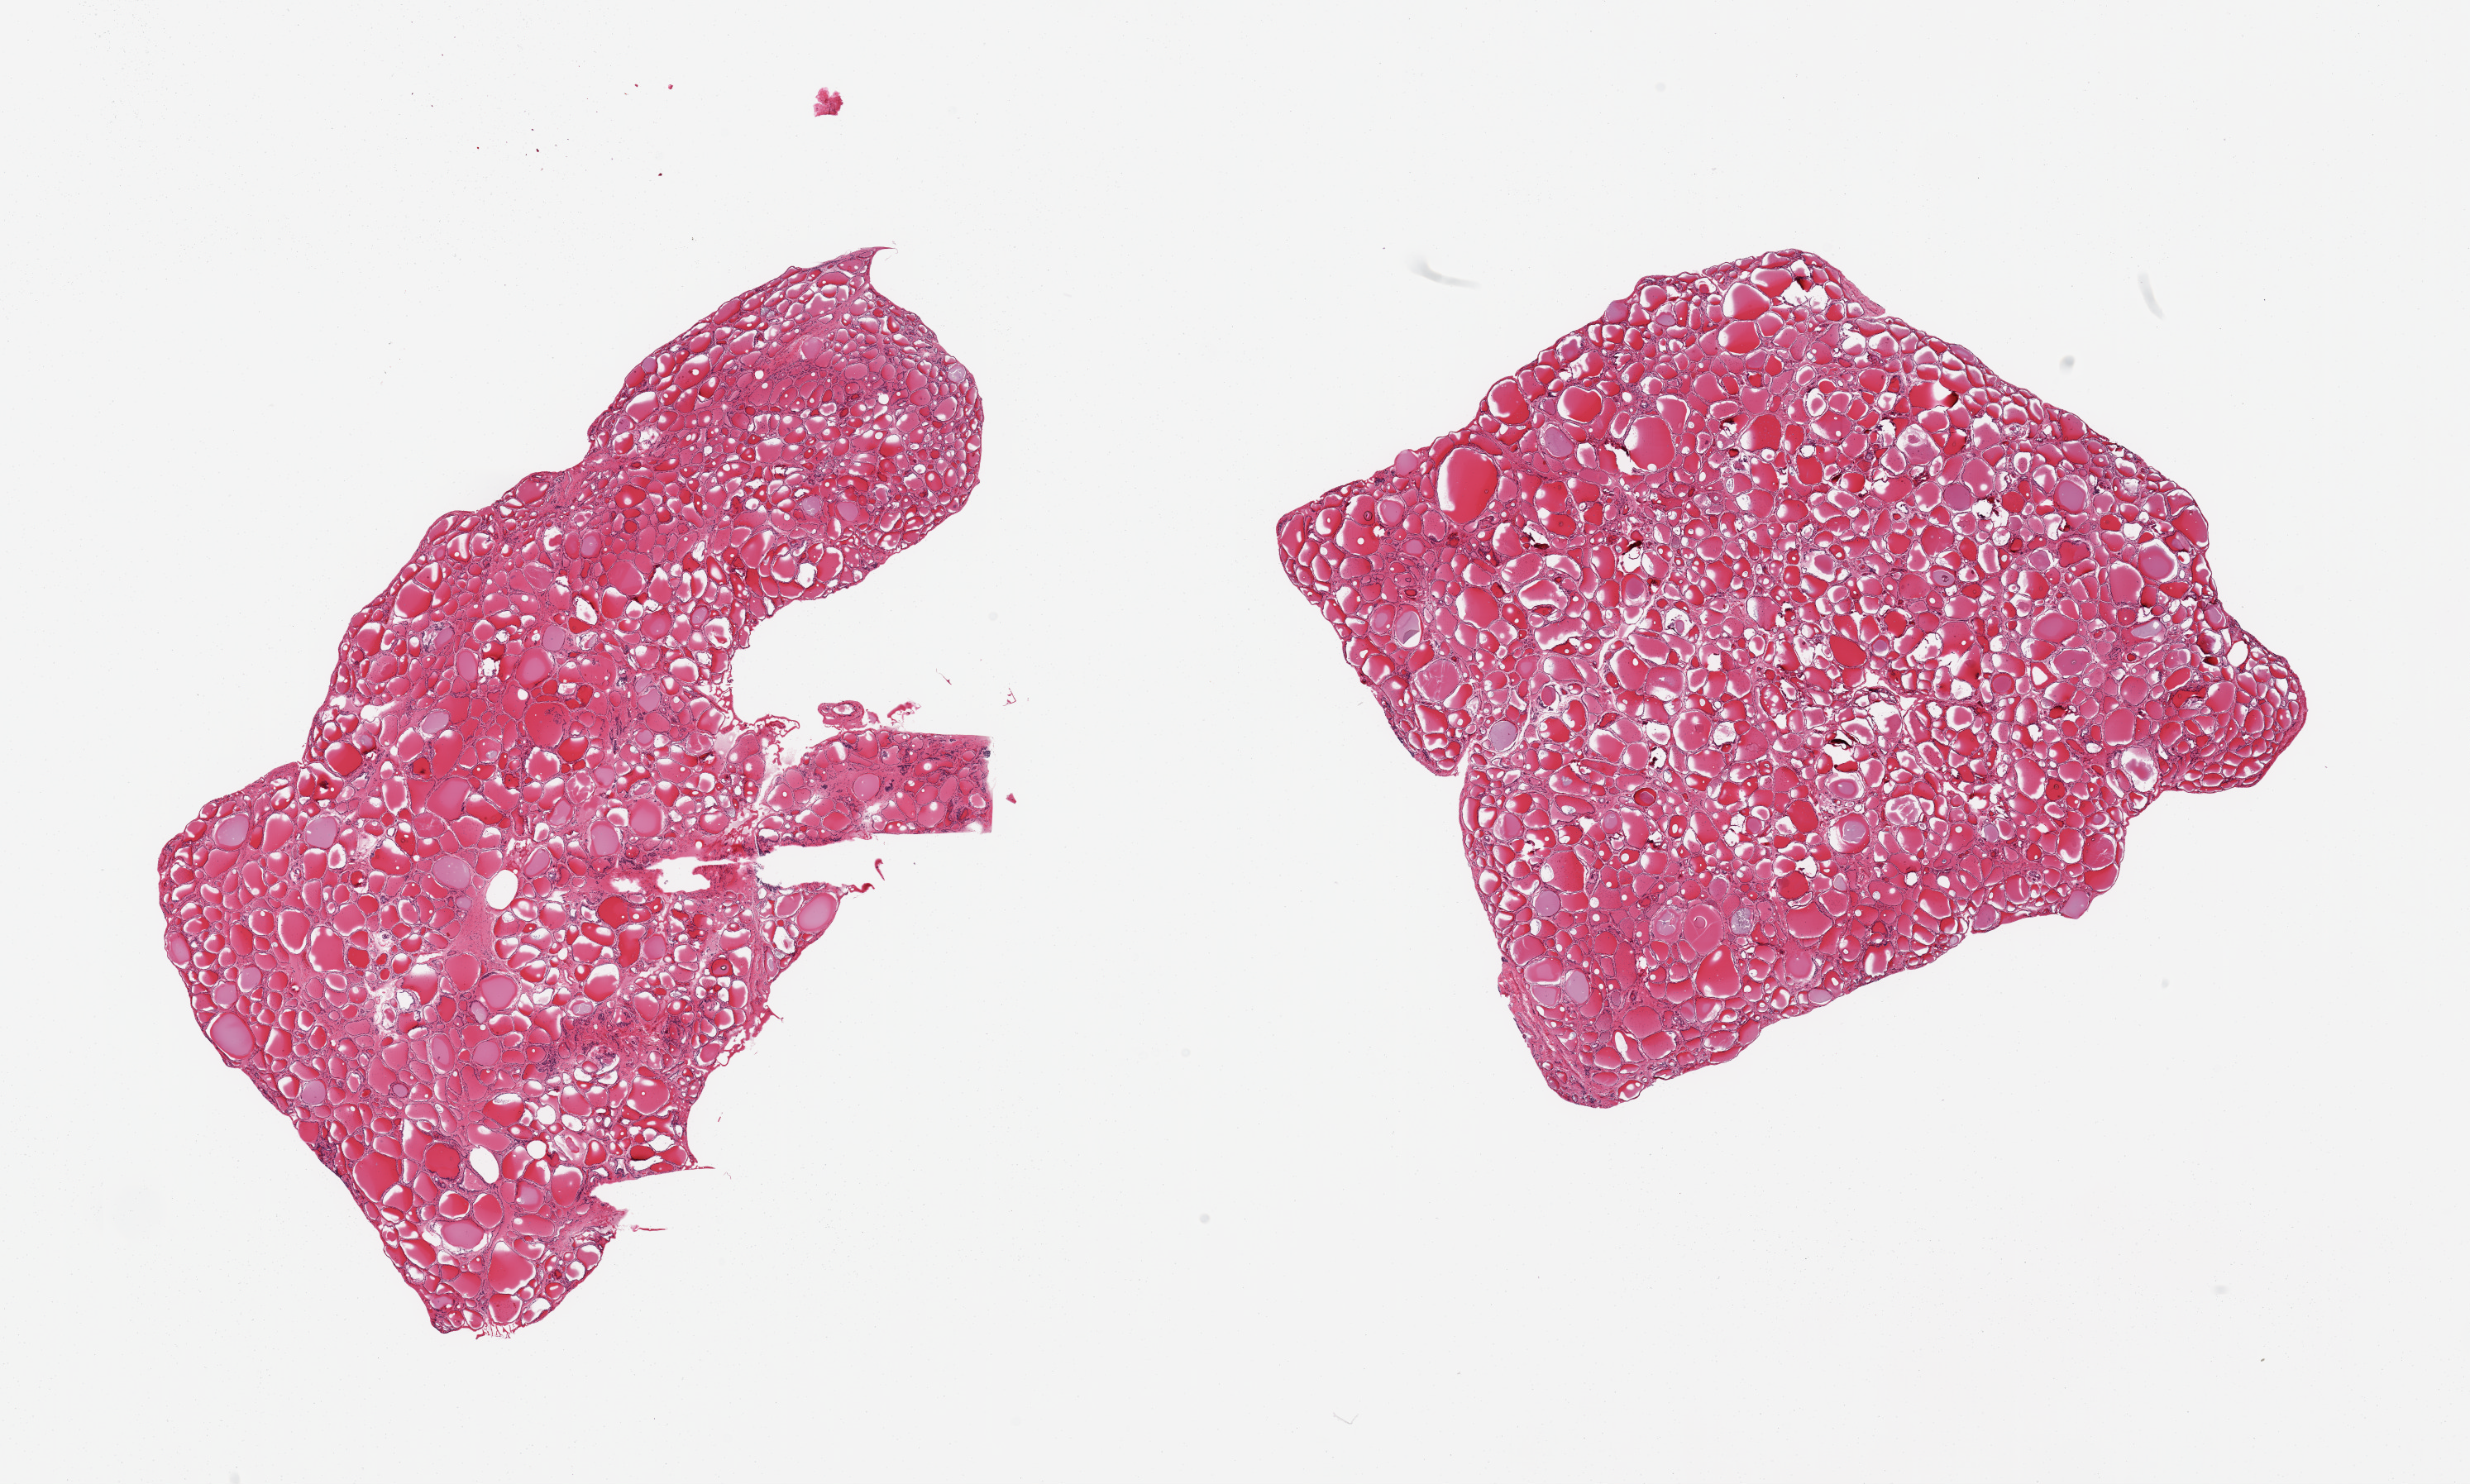
Hematoxylin and eosin (H&E) whole-slide image — shown as a low-resolution overview of the whole scanned area (about 23.6 x 14.2 mm), PAXgene-fixed paraffin-embedded (PFPE) section, sampled site (target tissue): thyroid, donor tissue sample. Donor: male.
Pathologist's review note for this sample: 2 pieces; no extraneous tissue.